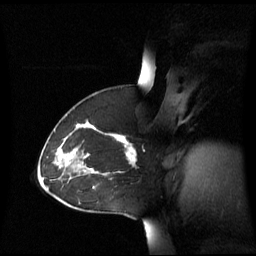
Breast MRI (dynamic contrast-enhanced), one sagittal slice. Position 40 of 60 along the scan axis. Dynamic contrast-enhanced series, image 2 of 3 at this slice position (ordered by acquisition). 1.5 T. TE 4.2 ms, TR 8.4 ms. 2.8 mm slice thickness. 256 × 256 image matrix, field of view 270 × 270 mm. Patient: female, 43 years. From the clinical record (not read from this slice): setting: breast cancer imaged before/during neoadjuvant chemotherapy; receptor status: triple-negative.
Structures marked on this image (semi-automatically segmented with operator editing):
- analysis volume of interest (the breast-tissue region the enhancement analysis was run in; not a lesion): bounding box (x1, y1, x2, y2) in pixels: (55, 124, 137, 173)
- tumour enhancement mask (voxels above the 70 % enhancement threshold inside the analysis volume of interest): (70, 136, 136, 165)